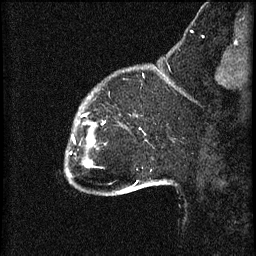
Breast MRI (dynamic contrast-enhanced), one sagittal slice. Slice 11 of 60 in the series (ordered by position). 3 images stored at this slice position (order not interpretable as contrast timing). 1.5 T. TE 4.2 ms, TR 8.2 ms. 2 mm slice thickness. 256 × 256 image matrix, field of view 180 × 180 mm. Female patient, age 32 years.
Structures marked on this image (semi-automatic segmentation, software-assisted and operator-edited):
- analysis volume of interest (the breast-tissue region the enhancement analysis was run in; not a lesion): box from (x=67, y=106) to (x=94, y=165) px
- tumour enhancement mask (voxels above the 70 % enhancement threshold inside the analysis volume of interest): (x=91, y=138)–(x=93, y=147)